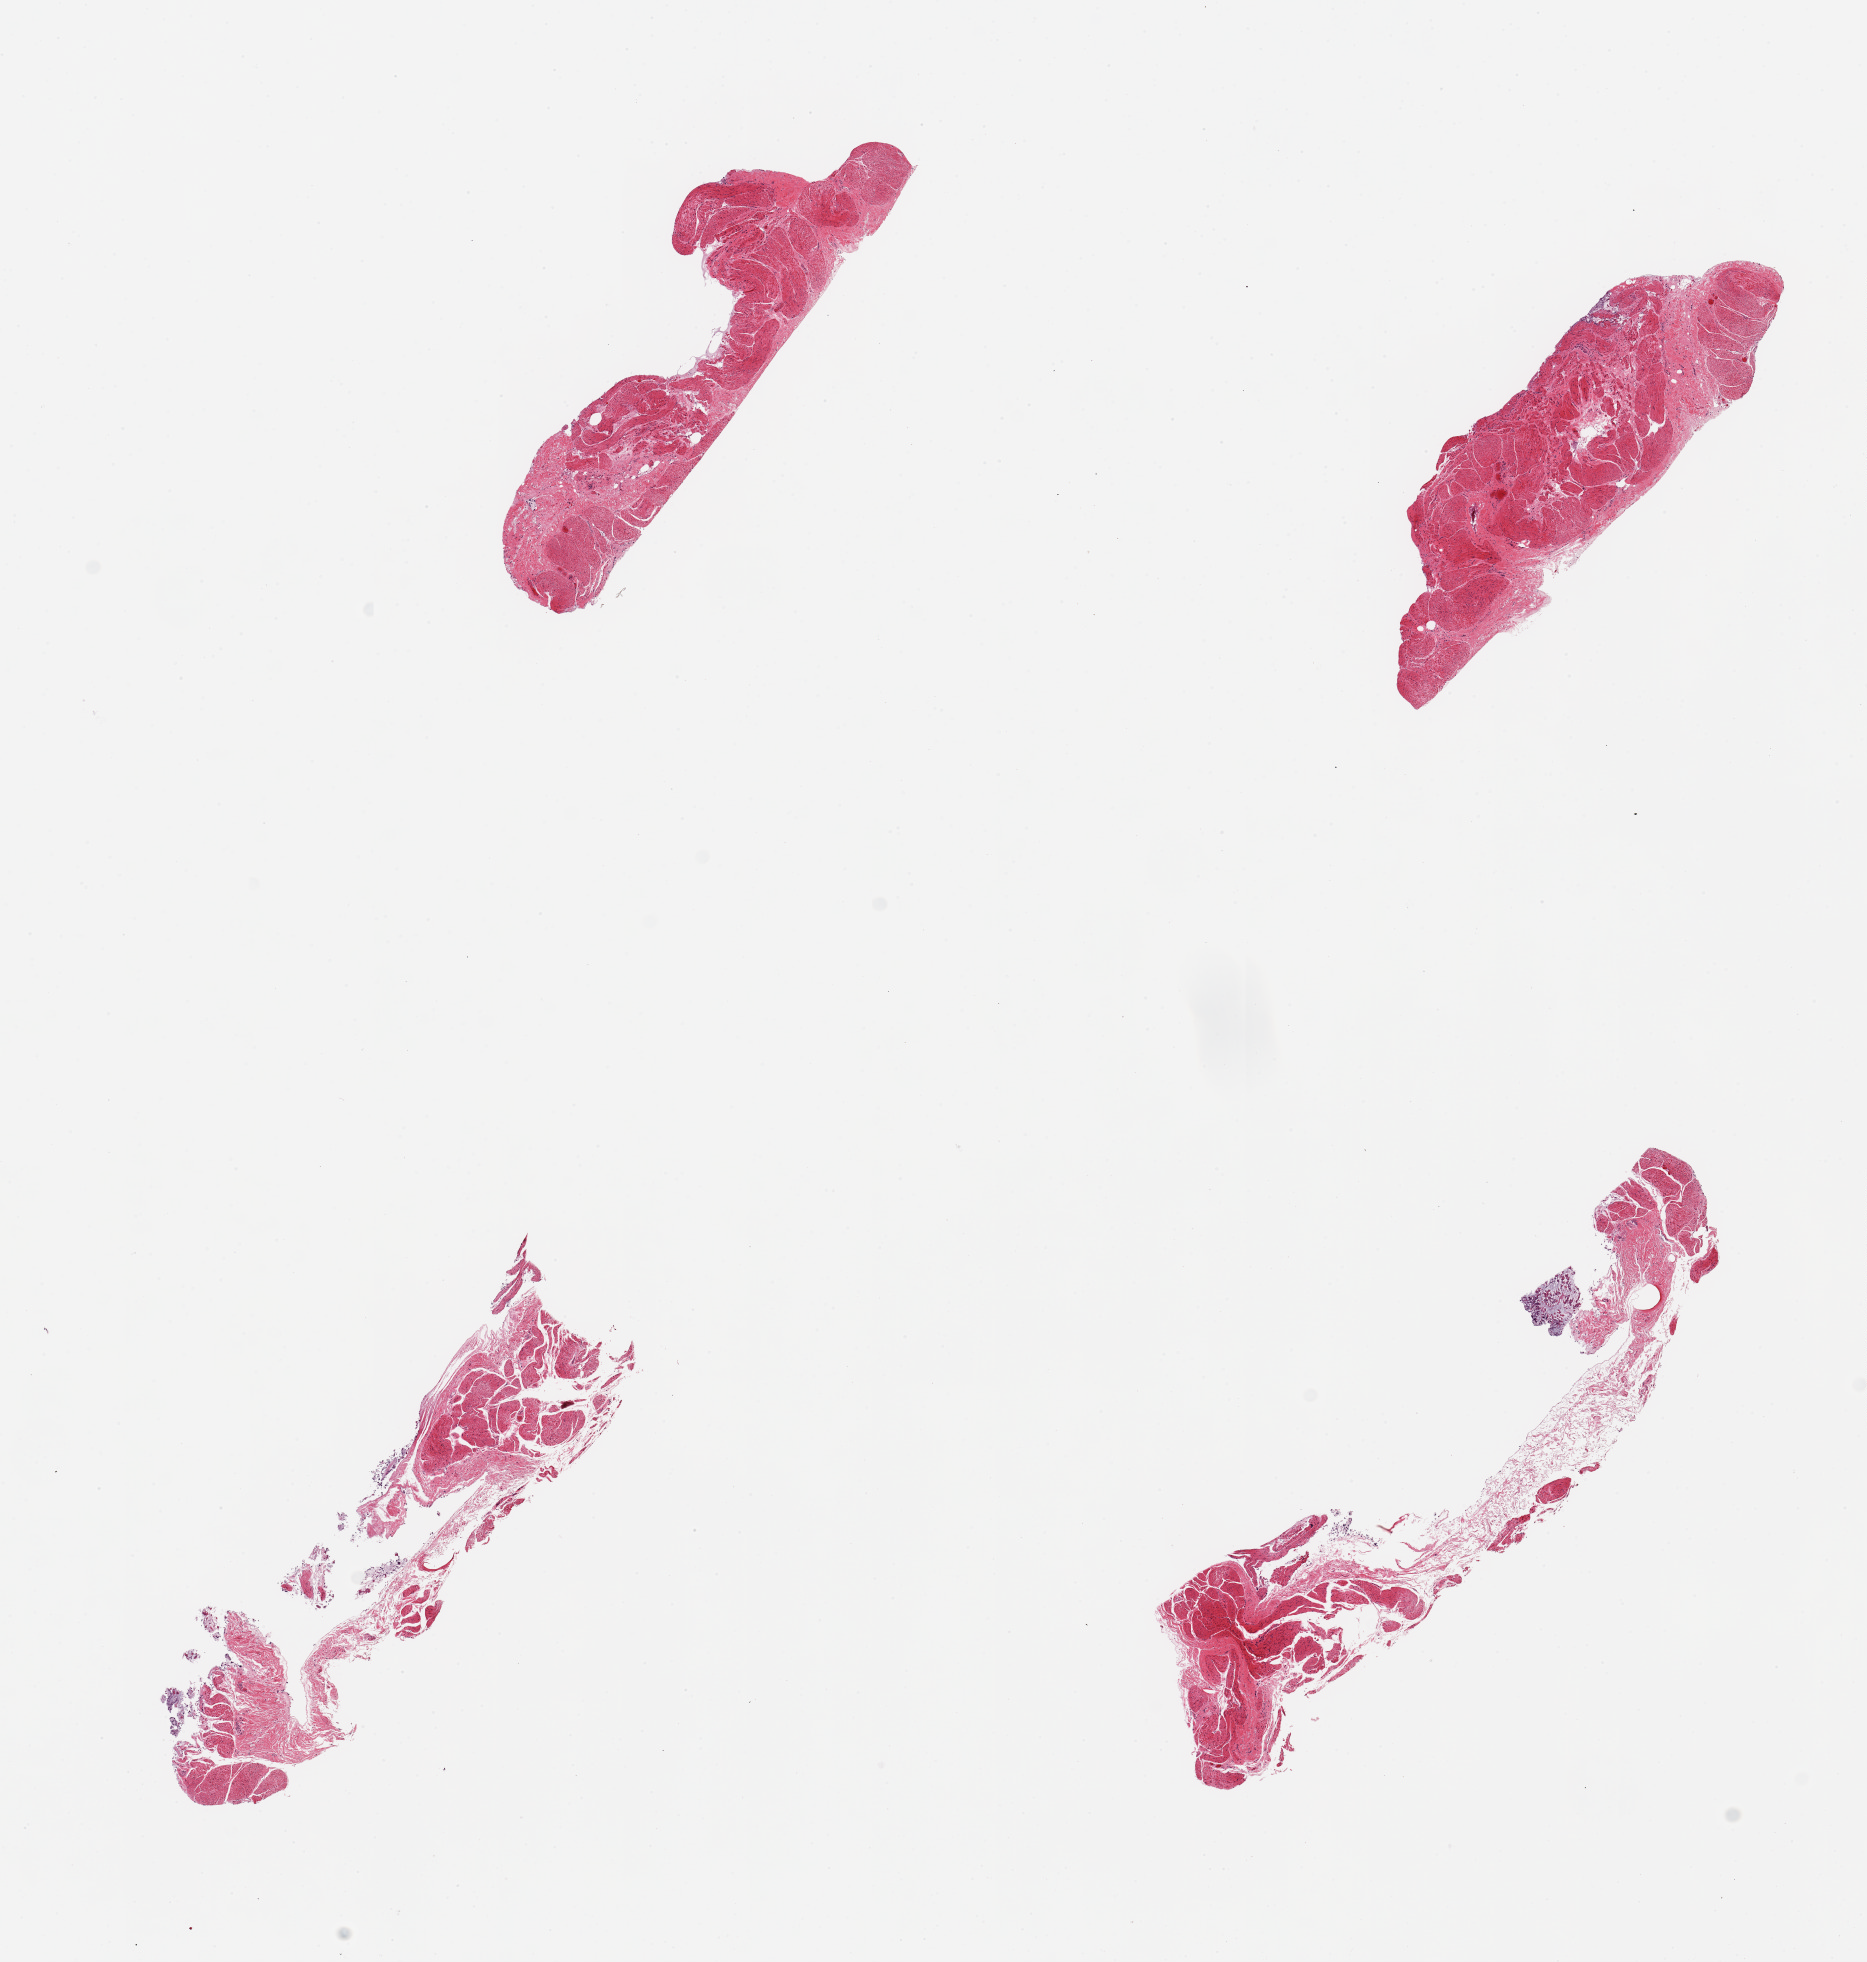
Digitized hematoxylin and eosin (H&E)-stained section, low-resolution overview of the scanned area, about 14.8 x 15.5 mm. PAXgene-fixed paraffin-embedded (PFPE) section. Target tissue: ileum. Donor tissue sample. Male donor.
Review note (as recorded): 4 pieces; mostly muscle, no lymphoid tissue.